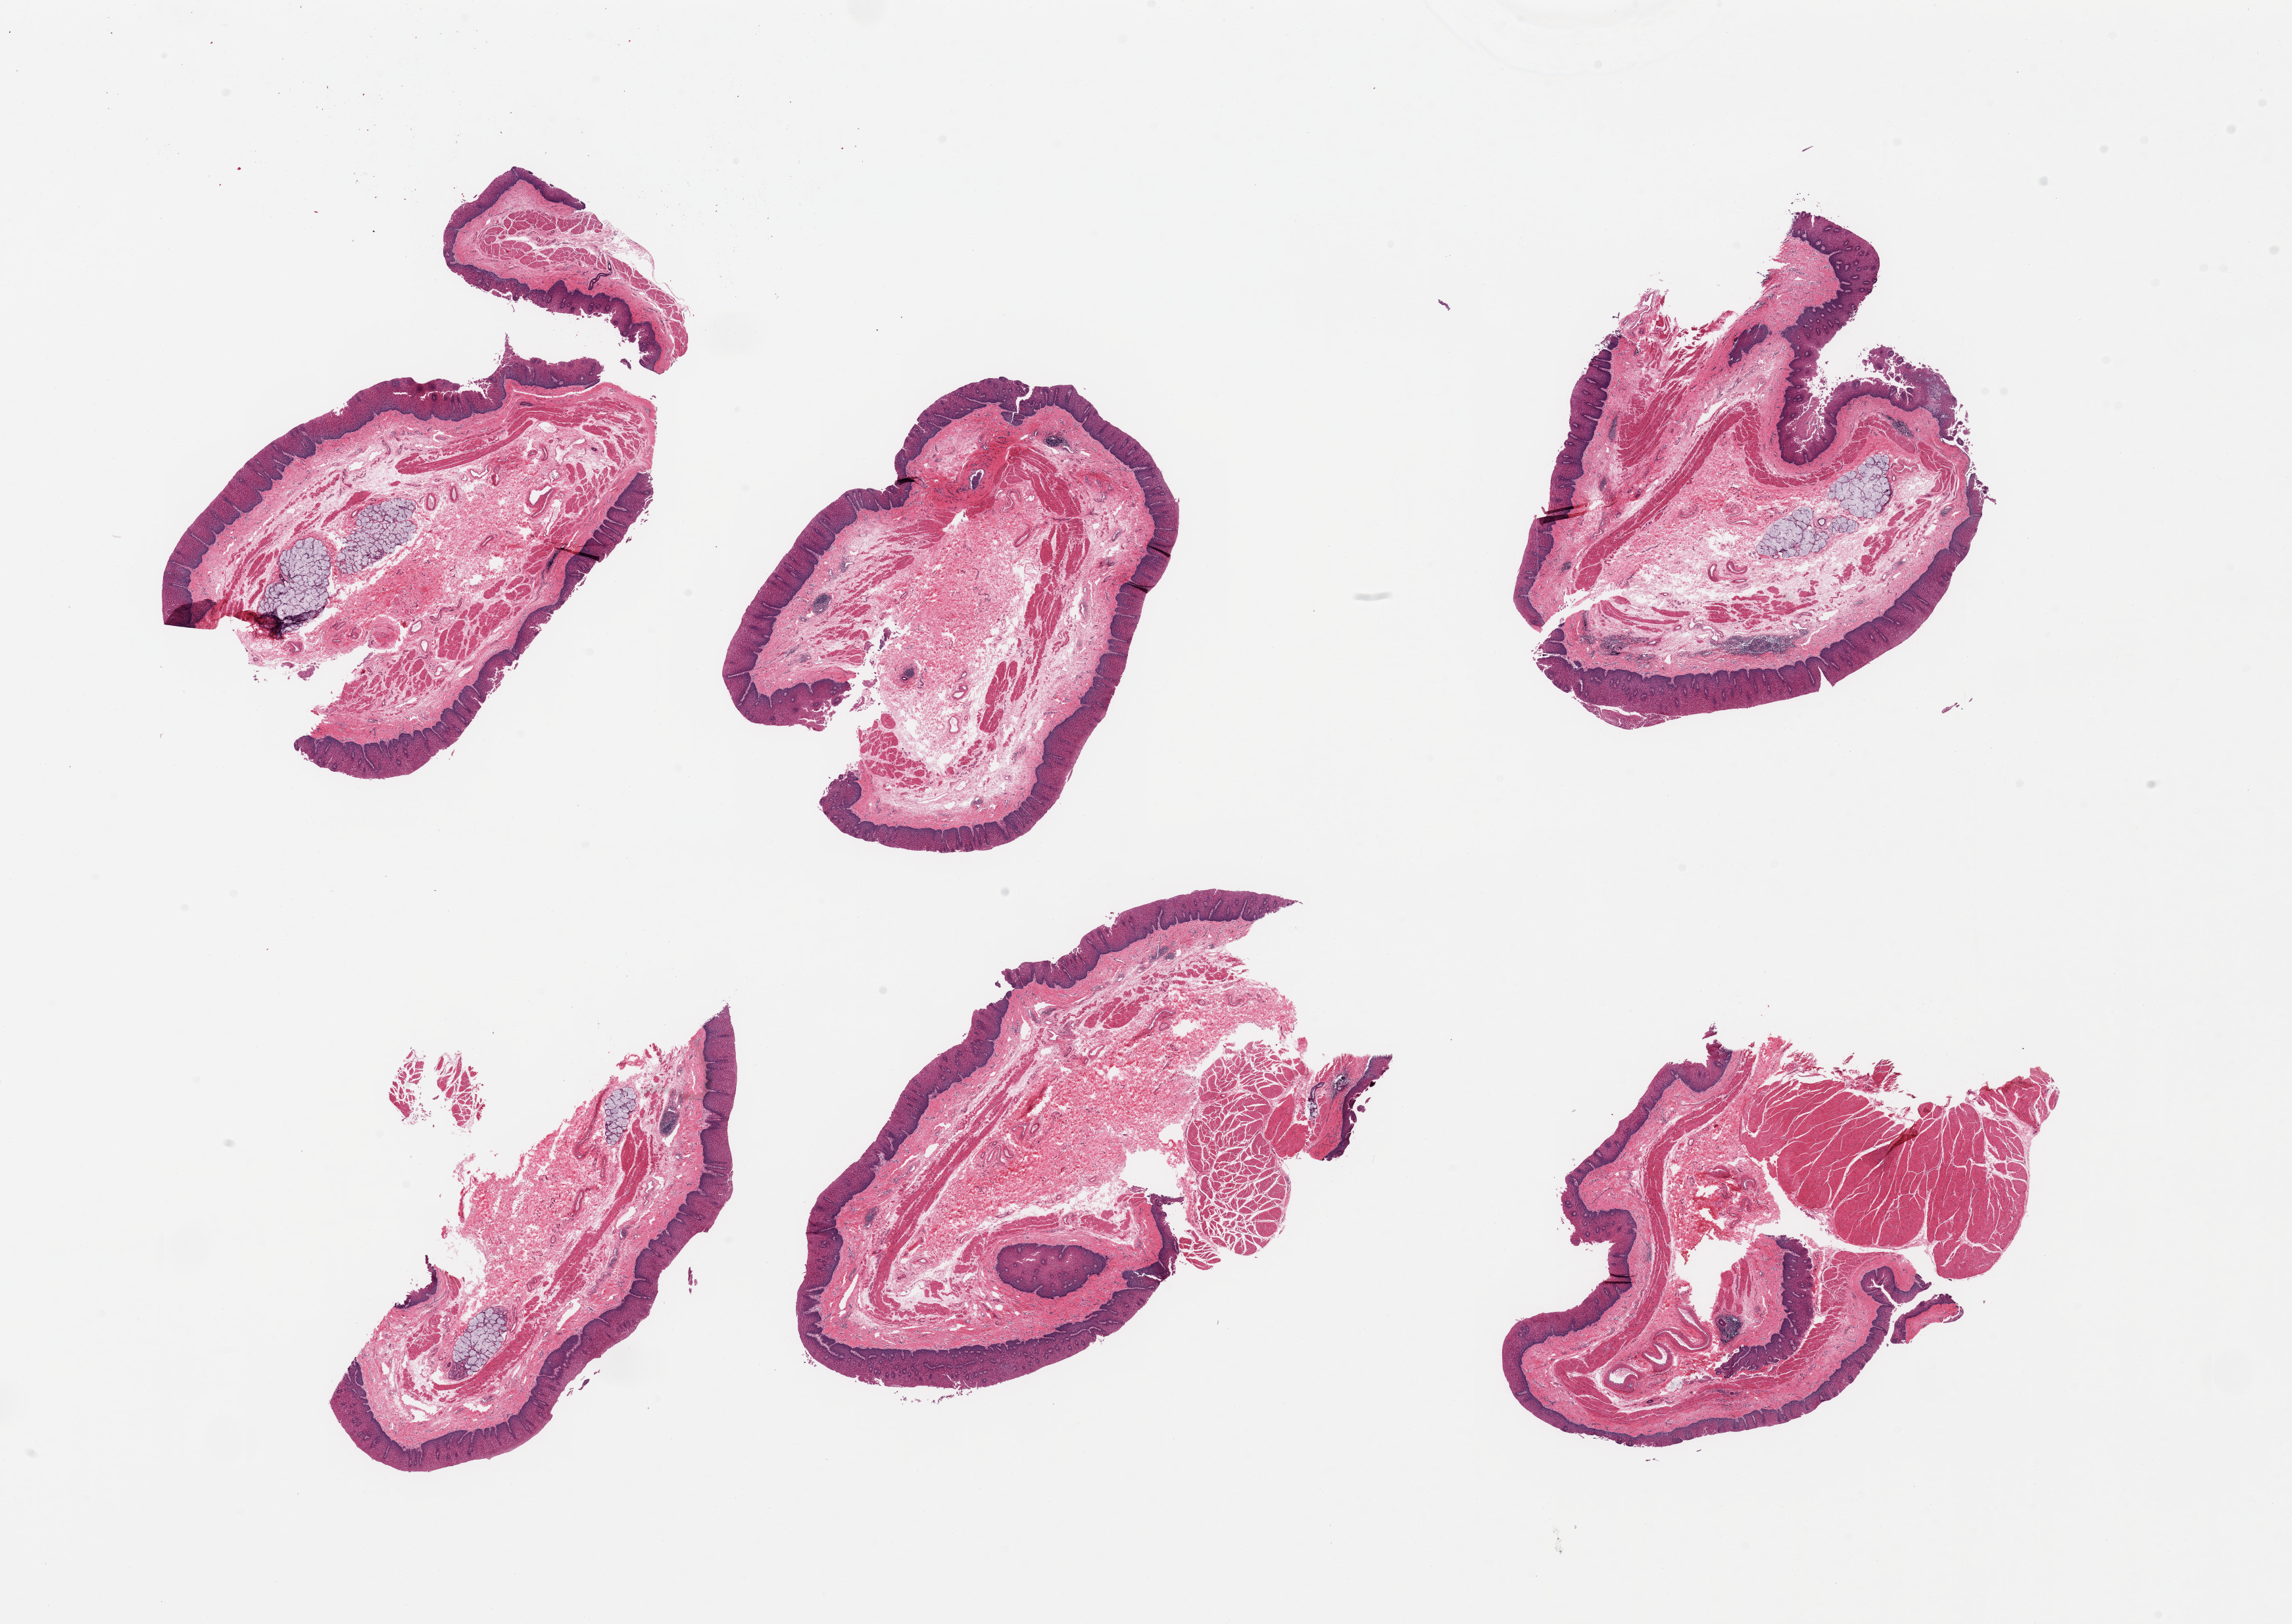
Whole-slide image, H&E stain, brightfield — whole scanned area (about 27.6 x 19.5 mm) shown as a low-resolution overview, PAXgene-fixed, paraffin-embedded tissue, sampled site (target tissue): esophageal mucous membrane, donor tissue sample.
Review note (as recorded): 6 pieces; submucosal glands in 3 pieces.